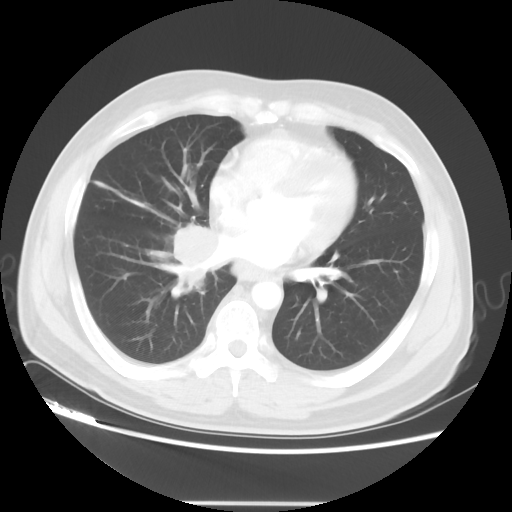
Chest CT, one axial slice. Position 19 of 48 along the scan axis. Lung window (W 1500 / L -600 HU). 5 mm slice thickness. 512 × 512 image matrix. Patient: male, 53 years. From the clinical record (not read from this slice): clinical TNM (as recorded): T2 N3 M0.
Structures marked on this image (rectangle marked by the reading radiologist):
- lung tumour (recorded histology: small cell carcinoma): bounding box <163,216,226,295> (left, top, right, bottom; pixels)